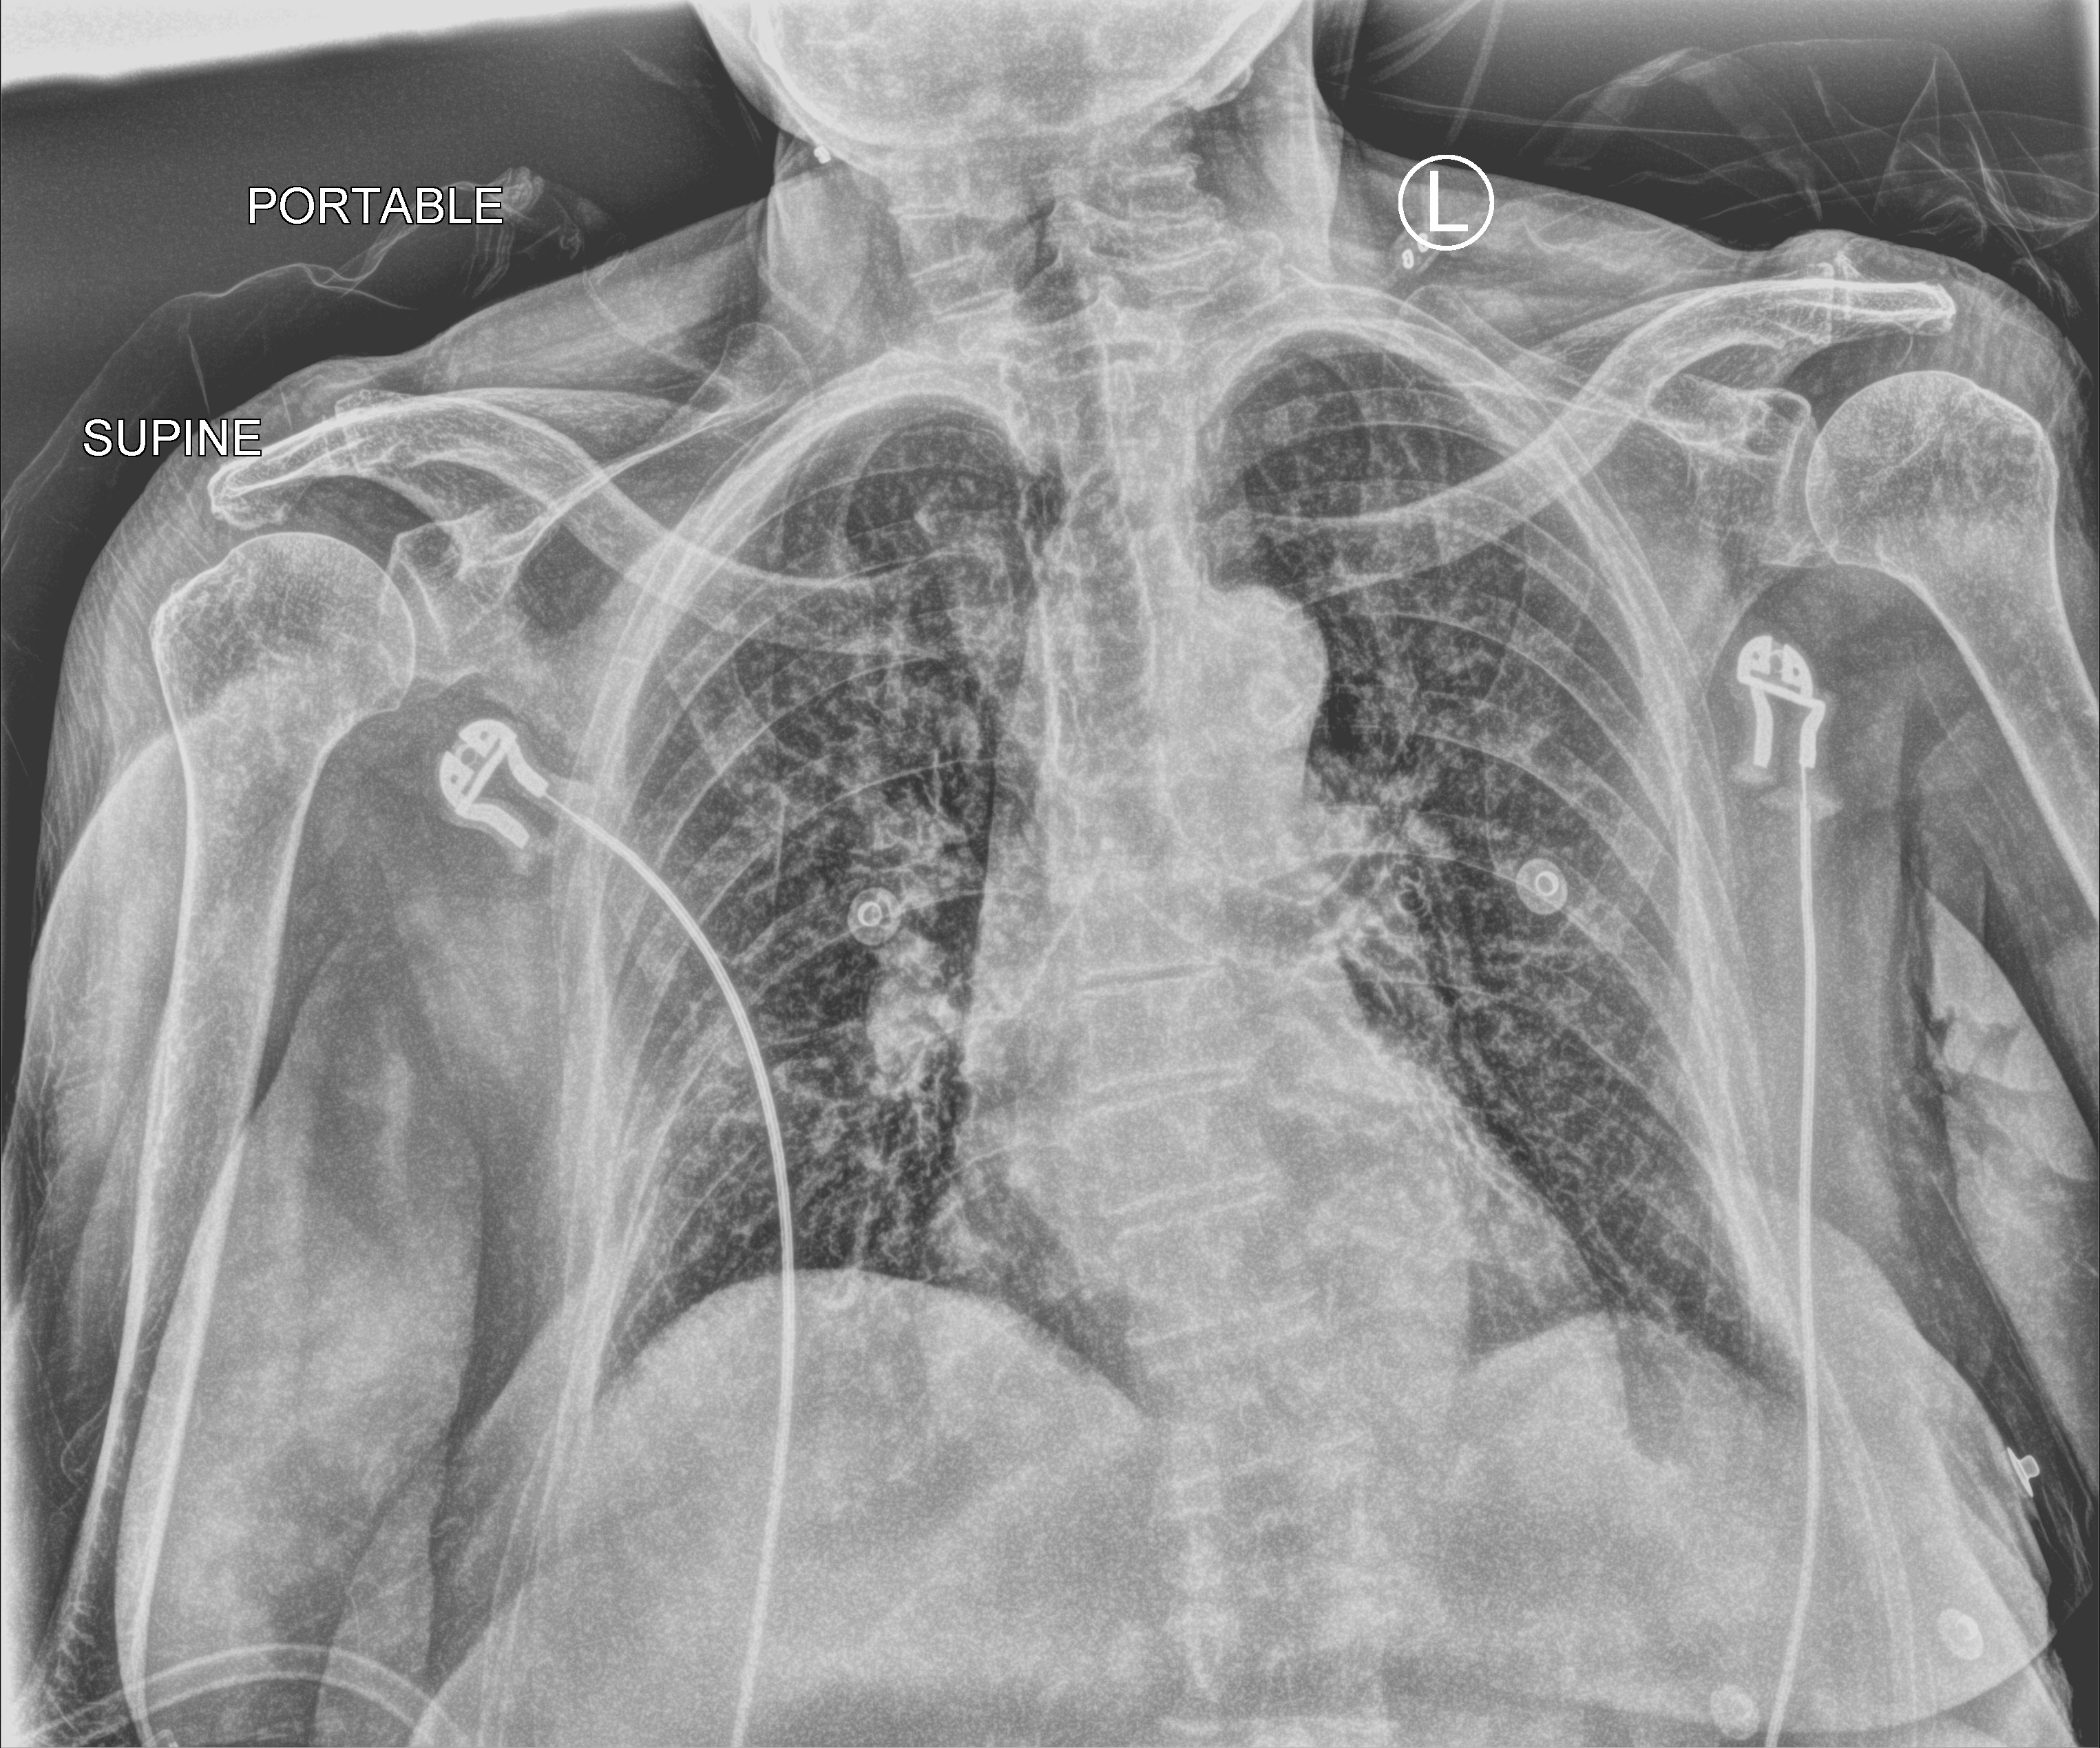
Chest X-ray (portable); anteroposterior (AP) projection. Patient hospitalised with COVID-19; female, aged 75–90 years.
Hospital-stay facts (about this admission, not read from this image; timing relative to this image not recorded):
- smoking status (admission record): never